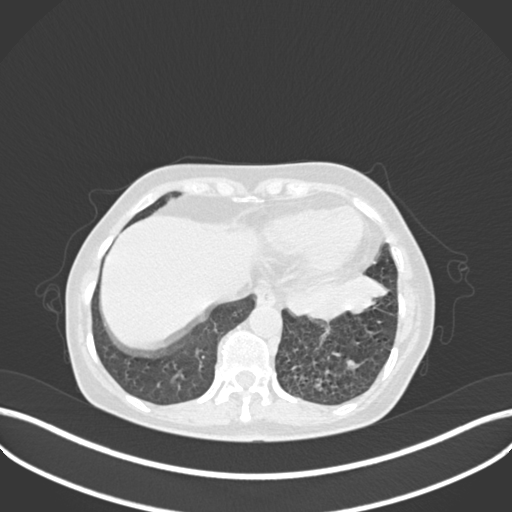
Chest CT, one axial slice; slice 55 of 270 in the series (ordered by position); reconstruction kernel B30f; 120 kVp; lung window (W 1500 / L -600 HU); 512 × 512 image matrix. Patient: female, 63 years. Case-level facts recorded for this patient, not image findings: clinical TNM (as recorded): T1b N0 M0.
Annotated regions visible in this slice (bounding box drawn by a radiologist):
- lung tumour (recorded histology: adenocarcinoma): bounding box (x1, y1, x2, y2) in pixels: (281, 268, 389, 321)